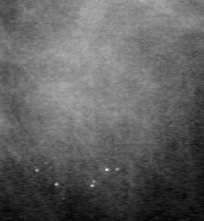
Cropped region of a digitized screen-film mammogram centred on a radiologist-marked abnormality, right breast, MLO view, BI-RADS breast density category 4 (scale 1–4).
Finding: mass, shape lobulated, margins circumscribed; BI-RADS assessment category 4; subtlety rating 3 on a 1 (subtle) to 5 (obvious) scale; pathology result (as recorded, not read from the image): benign.